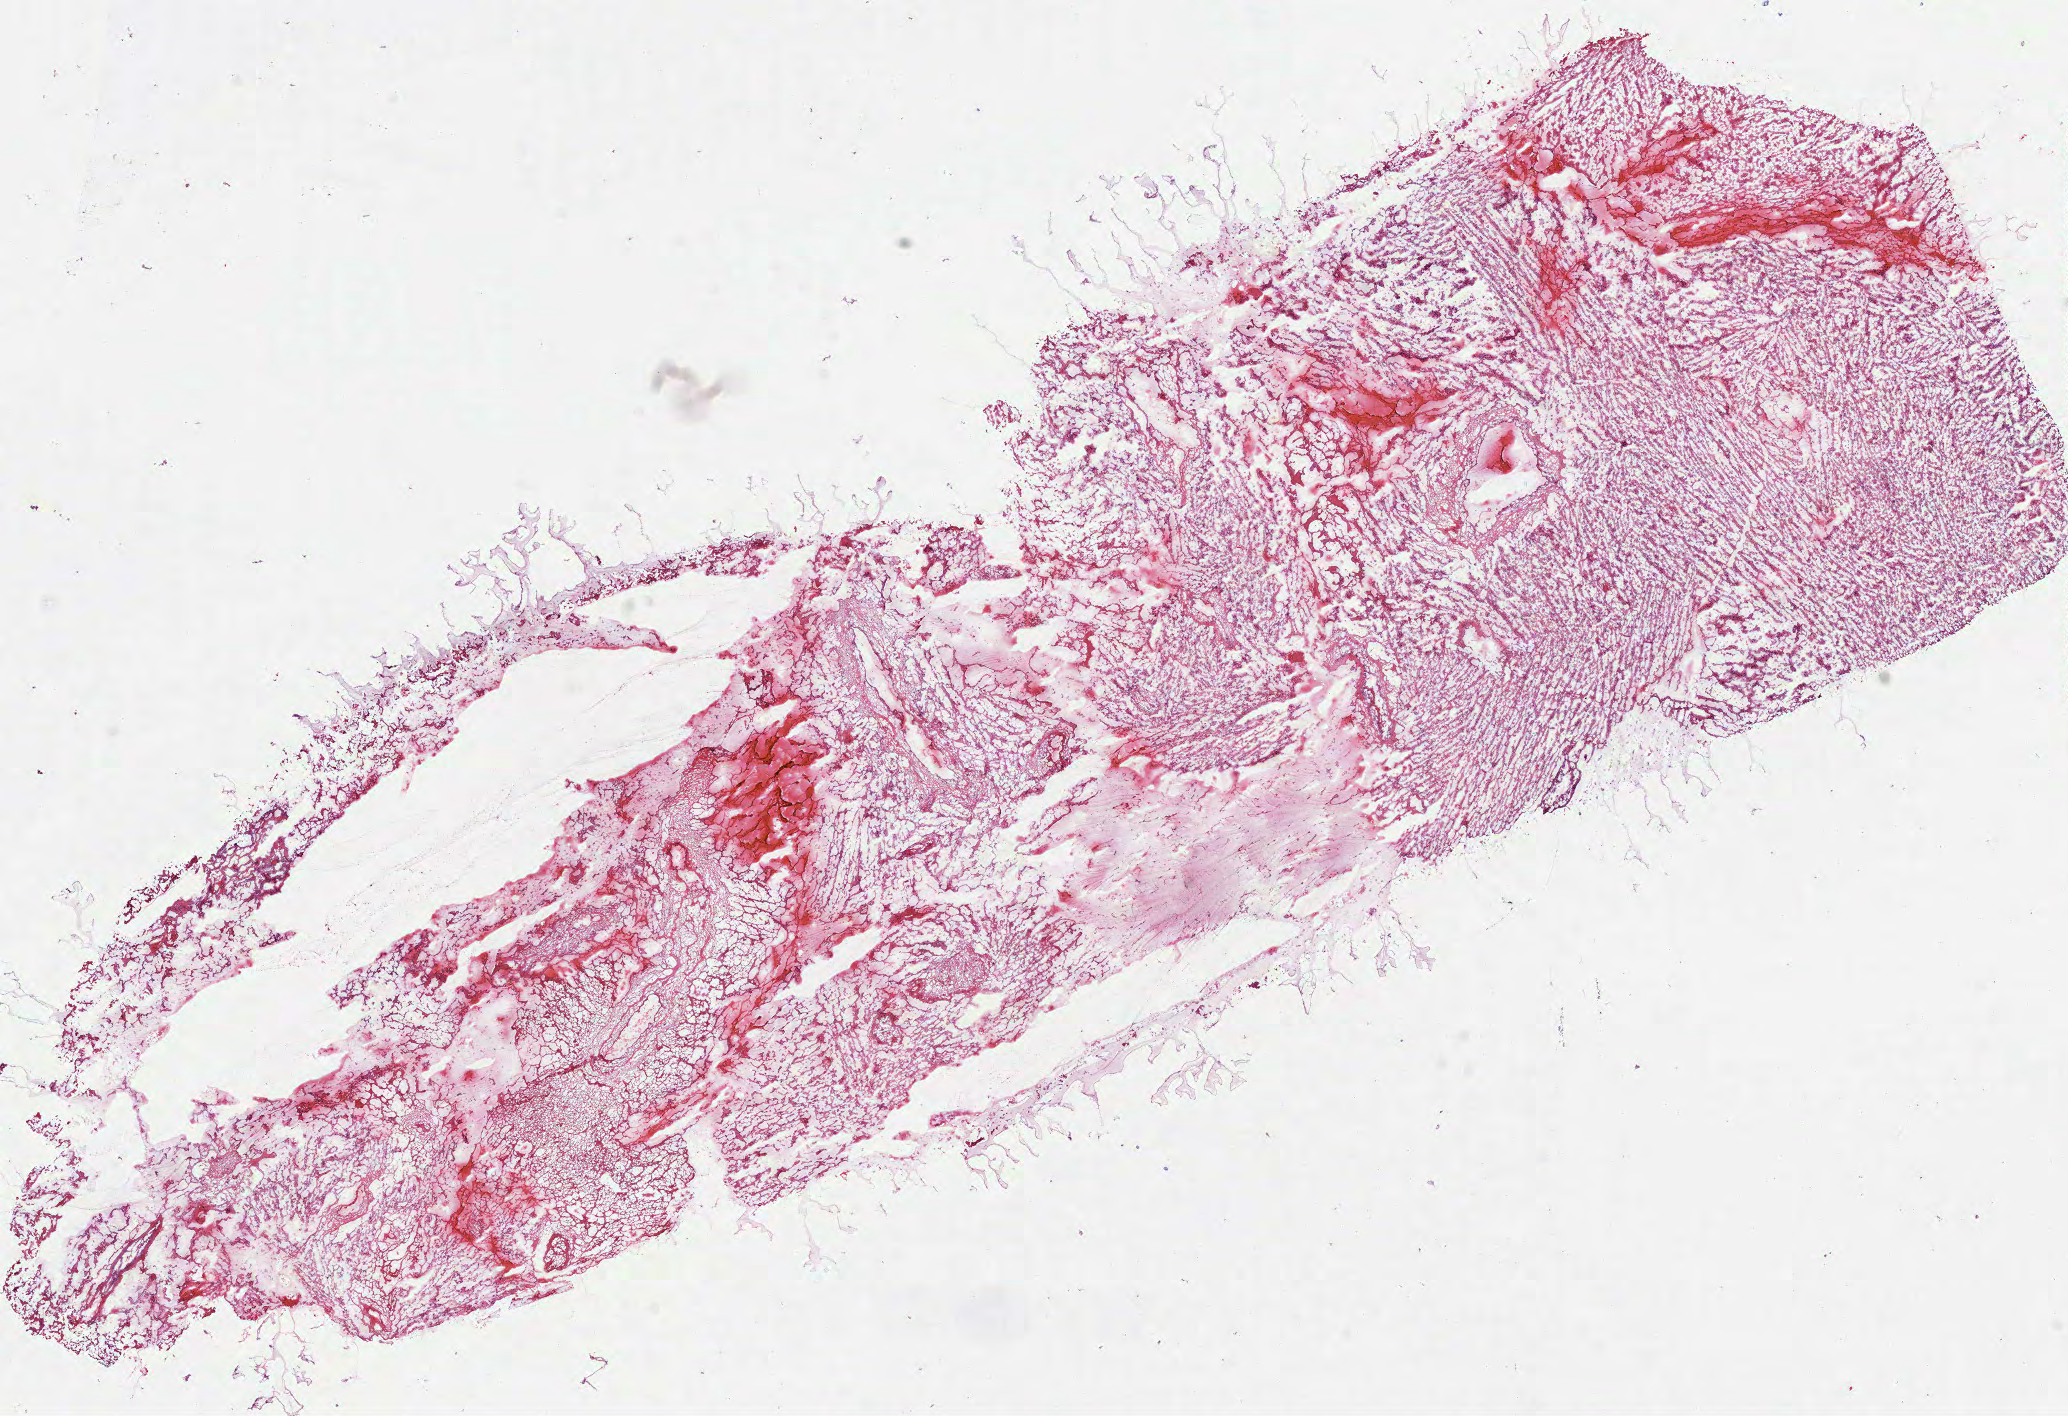
Digitized H&E tissue section (whole slide) — shown as a low-resolution overview of the whole scanned area (about 16.7 x 11.4 mm, from a 40x scan). Frozen section from the top of the tissue portion. Brain, primary tumour sample. Patient: male, age at initial diagnosis 74 years. Slide review estimates, as recorded: tumour cells 90%, tumour nuclei 70%, normal cells 0%, stromal cells 5%, necrosis 5%.
• pathologic diagnosis: Glioblastoma